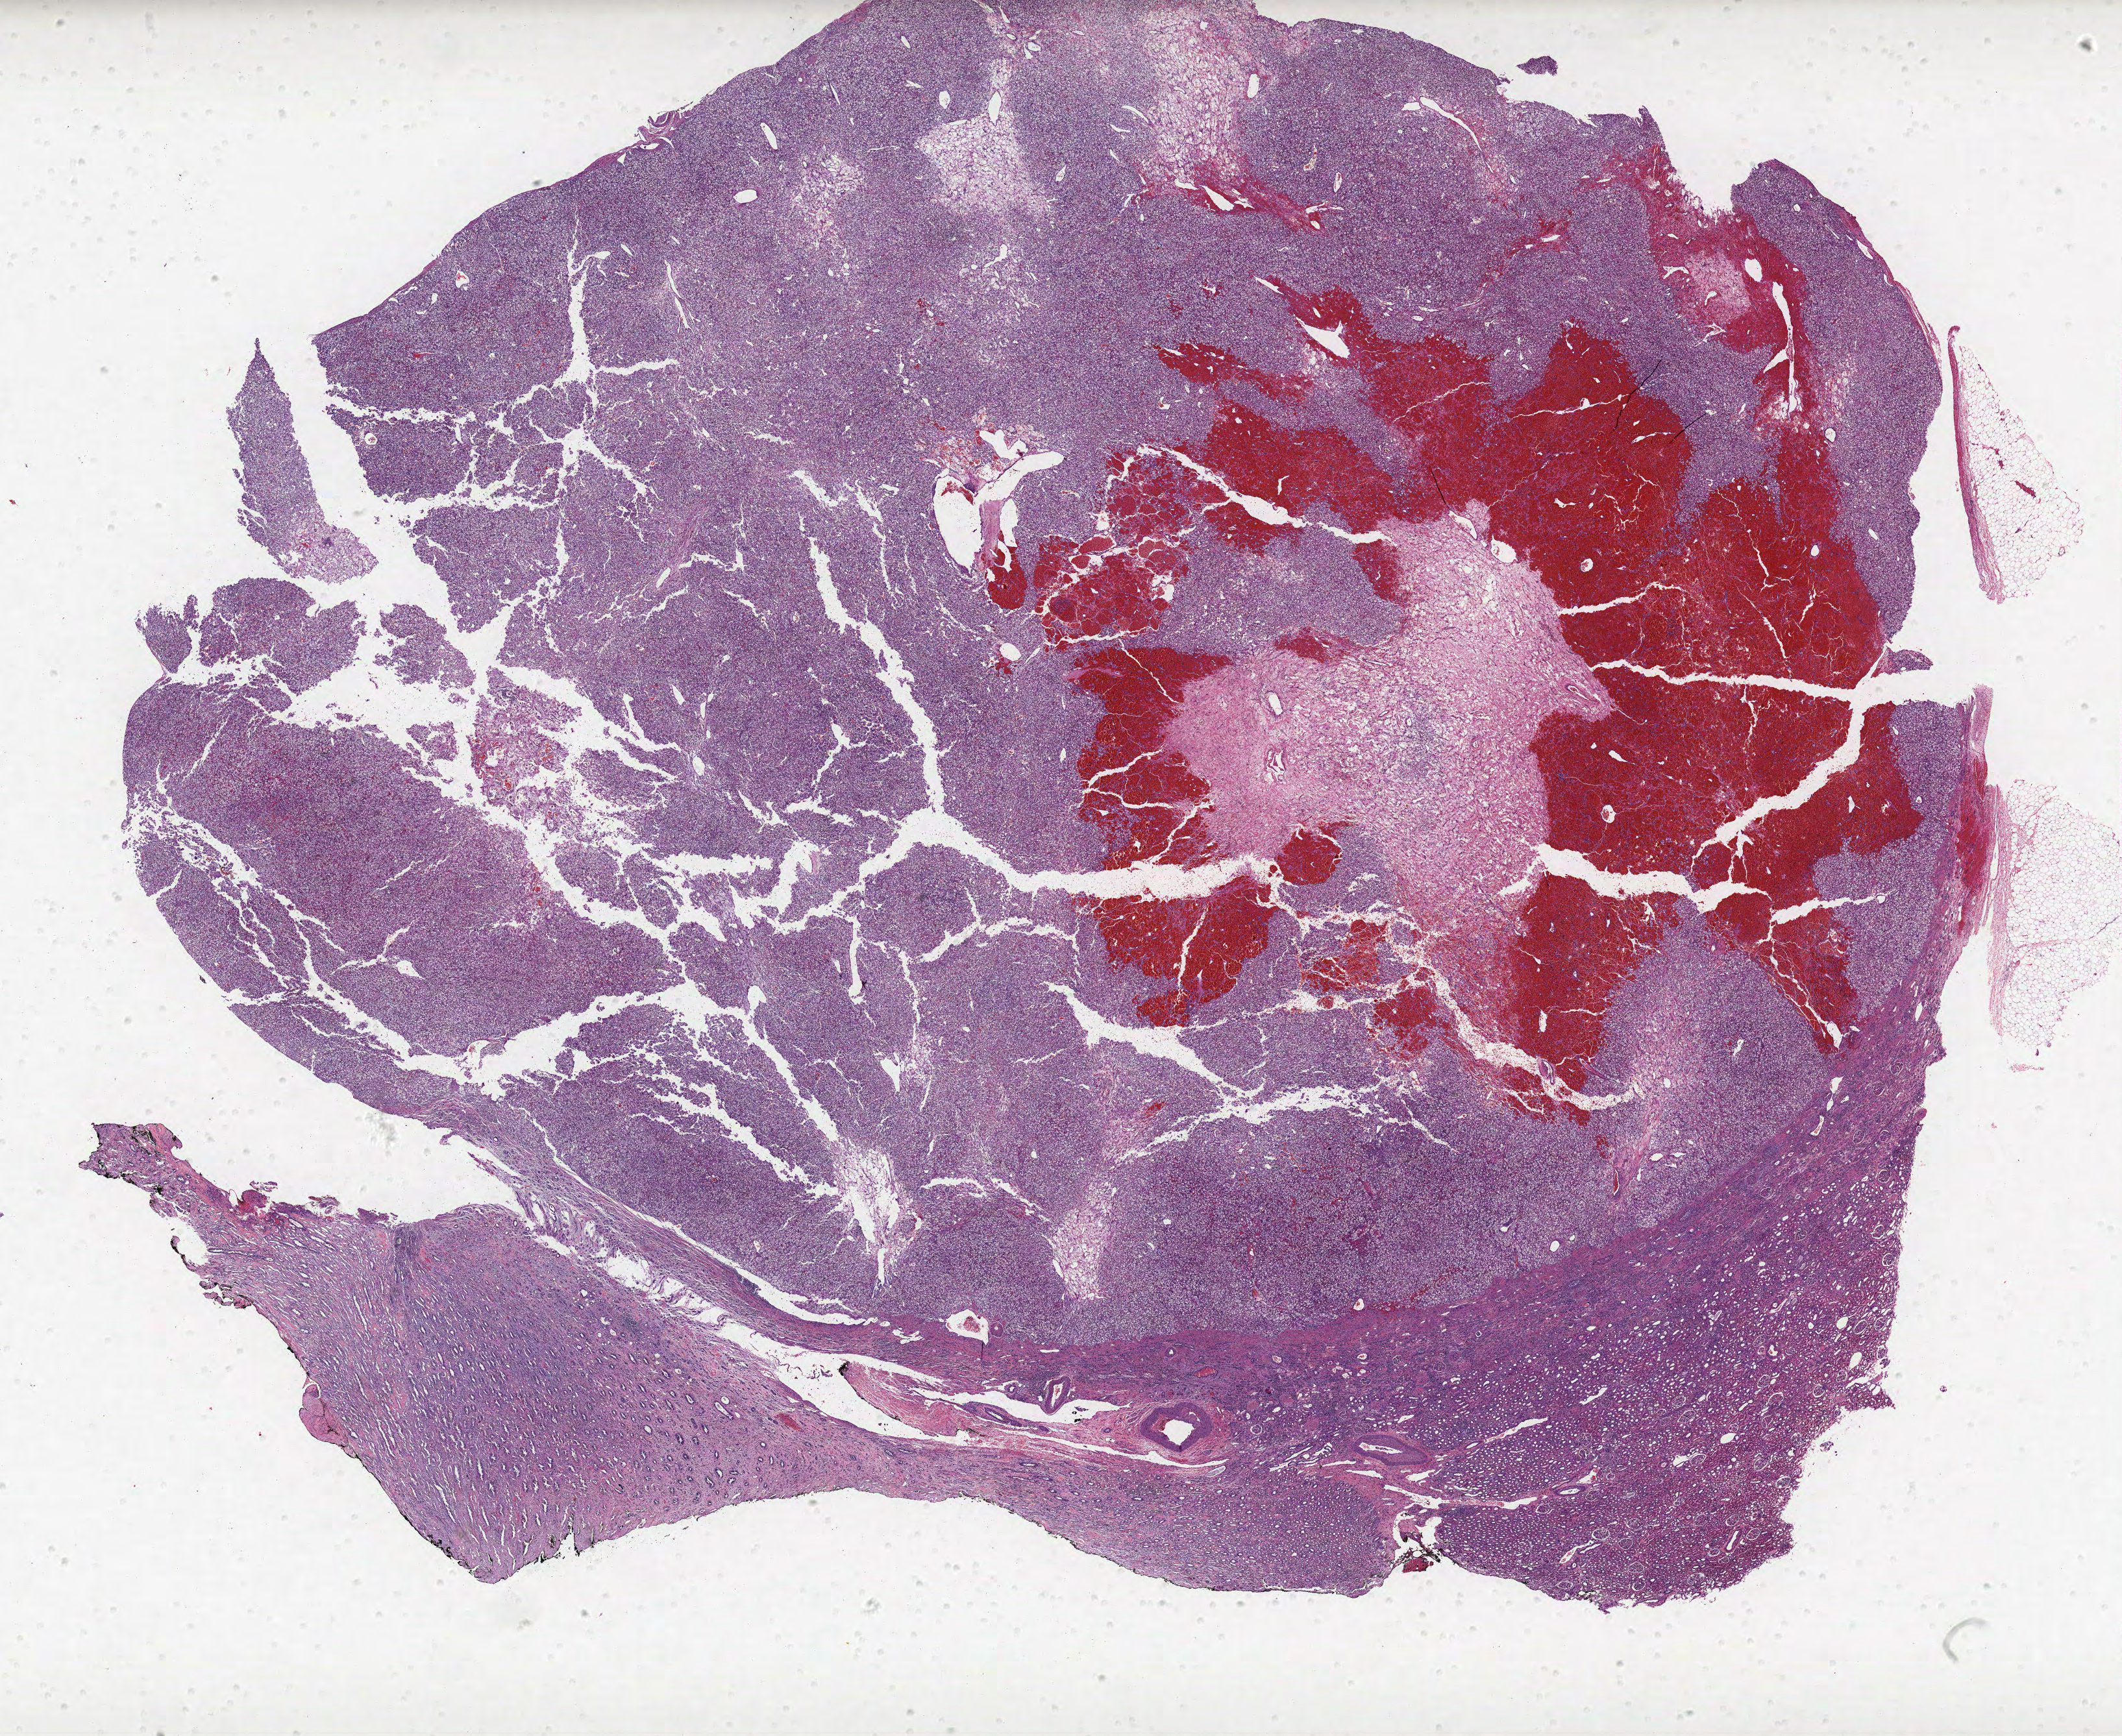
H&E whole-slide image — a low-resolution overview of the entire scanned area, about 26.1 x 21.4 mm, formalin-fixed paraffin-embedded (FFPE) diagnostic section, primary tumour sample from the kidney. Patient: male, age at initial diagnosis 61 years. Histologic grade: G2 (moderately differentiated).
TNM: T1a N0 M0. Lymph nodes positive (case pathology): 0 of 2 examined. Laterality: left. AJCC pathologic stage: I. Diagnosis: Clear cell adenocarcinoma, NOS.